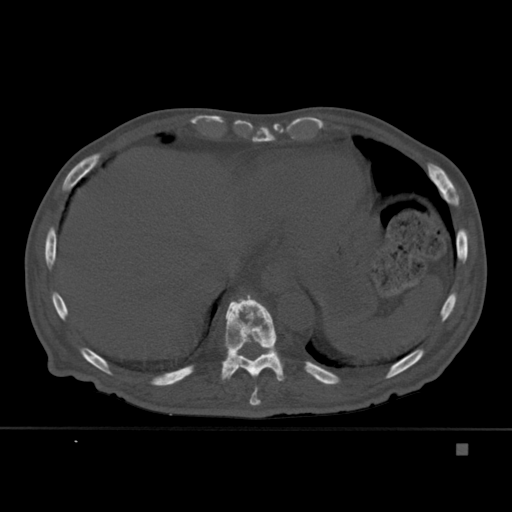
CT including the spine, one axial slice; slice 233 of 451 in the series (ordered by position); bone window (W 1800 / L 400 HU); 512 × 512 image matrix. Male patient, age 75 years. Case-level facts recorded for this patient, not image findings: primary cancer: prostate.
Annotated regions visible in this slice (semi-automatic segmentation, software-assisted and operator-edited):
- T10 vertebra: bounding box <221,295,286,382> (left, top, right, bottom; pixels)
- T11 vertebra: <268,350,275,353>
- T9 vertebra: <249,386,261,406>